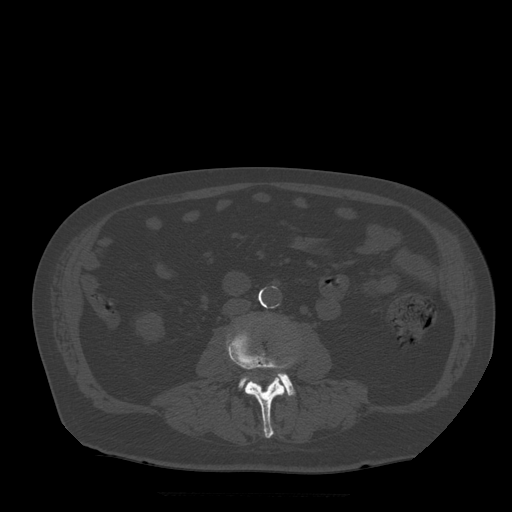
CT including the spine, one axial slice. Bone window (W 1800 / L 400 HU). 1.25 mm slice thickness. 512 × 512 image matrix, field of view 420 × 420 mm. Patient age 72 years. From the clinical record (not read from this slice): primary cancer: prostate.
Outlined on this slice (semi-automatically segmented with operator editing):
- L3 vertebra: bounding box <226,329,296,438> (left, top, right, bottom; pixels)
- L4 vertebra: <239,374,295,396>